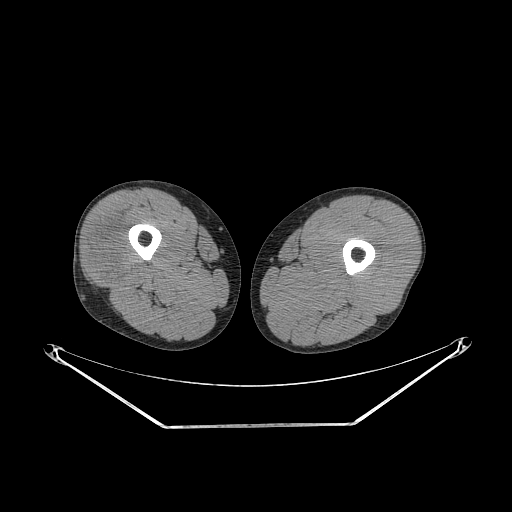
CT of an extremity soft-tissue mass (from a PET/CT study), one axial slice; position 230 of 267 along the scan axis; reconstruction kernel STANDARD; soft-tissue window (W 400 / L 40 HU); 512 × 512 image matrix, field of view 500 × 500 mm. Male patient. Case-level facts recorded for this patient, not image findings: histological type: poorly differentiated synovial sarcoma; grade: high; site of the primary tumour: right buttock.
Outlined on this slice (expert contour drawn on MRI and transferred to this co-registered scan by the dataset authors):
- gross tumour volume including surrounding oedema: bounding box [x1, y1, x2, y2] px = [89, 228, 140, 284]
- gross tumour volume (mass): [91, 231, 127, 280]